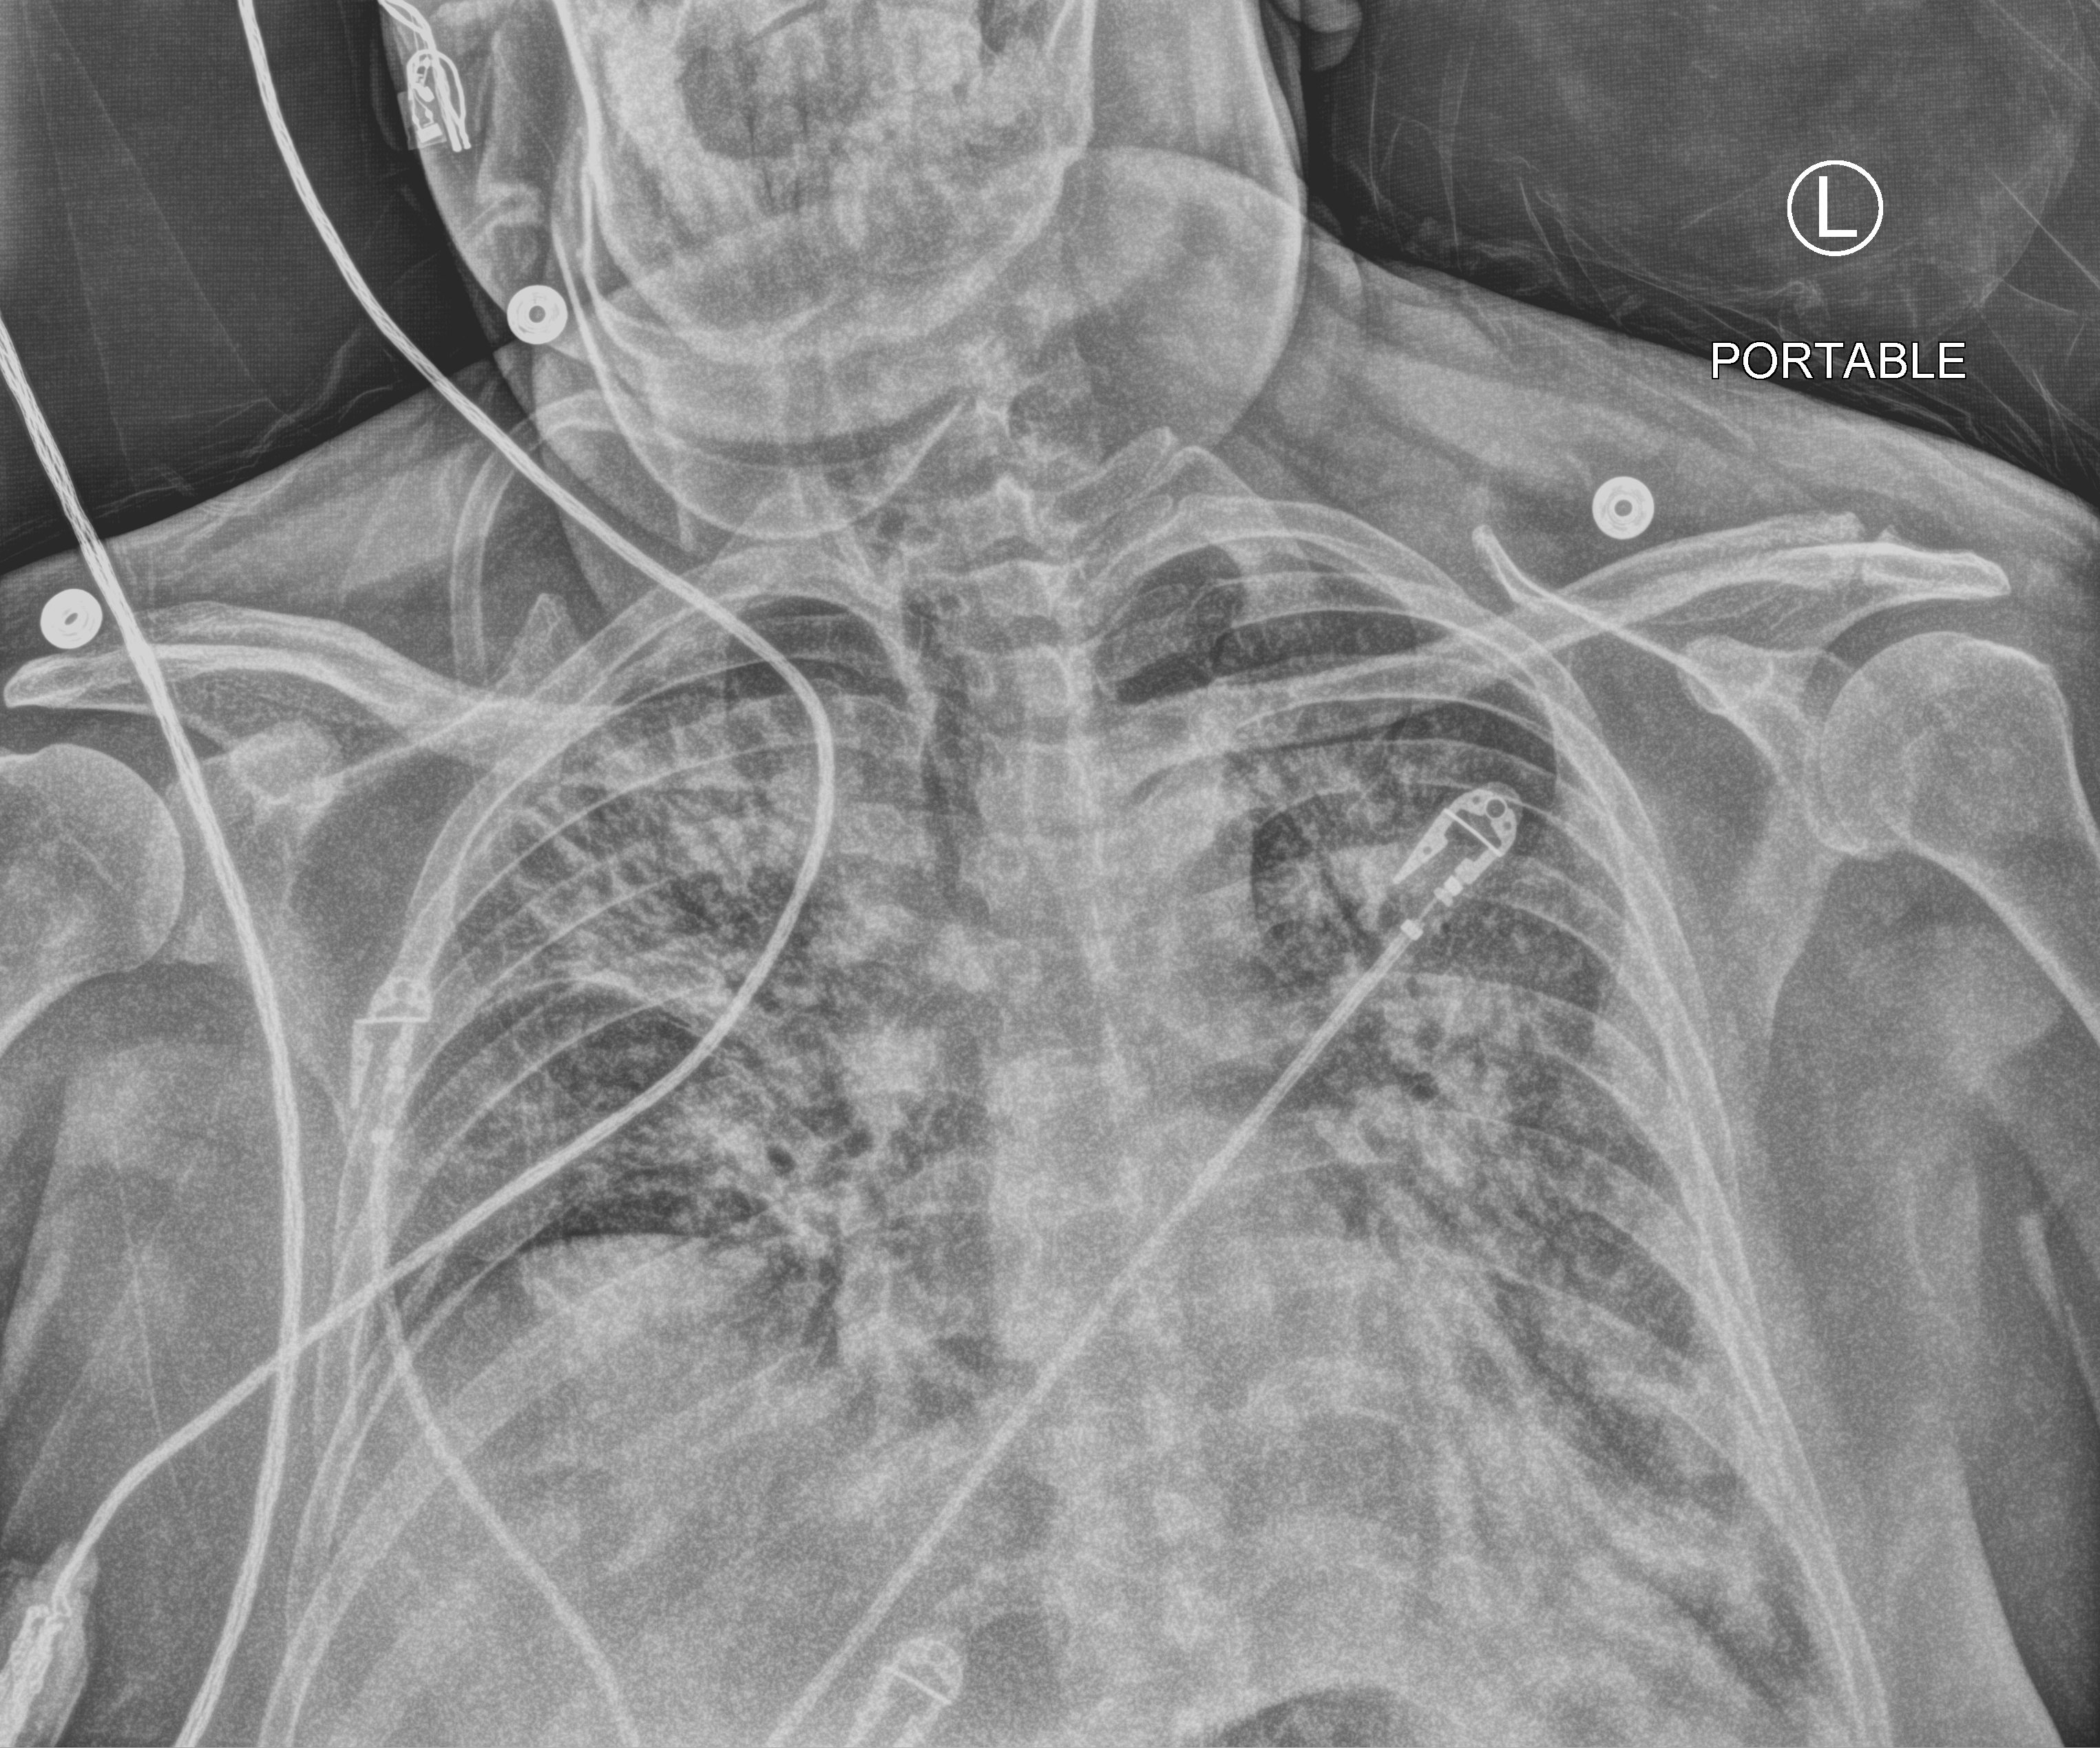
Portable chest radiograph; anteroposterior (AP) projection. Male patient hospitalised with COVID-19, age 18–59 years.
Admission-level facts for this patient (not findings on this image; timing relative to this image not recorded): diabetes (admission record): no; mechanically ventilated during this hospital stay: yes; smoking status (admission record): never.